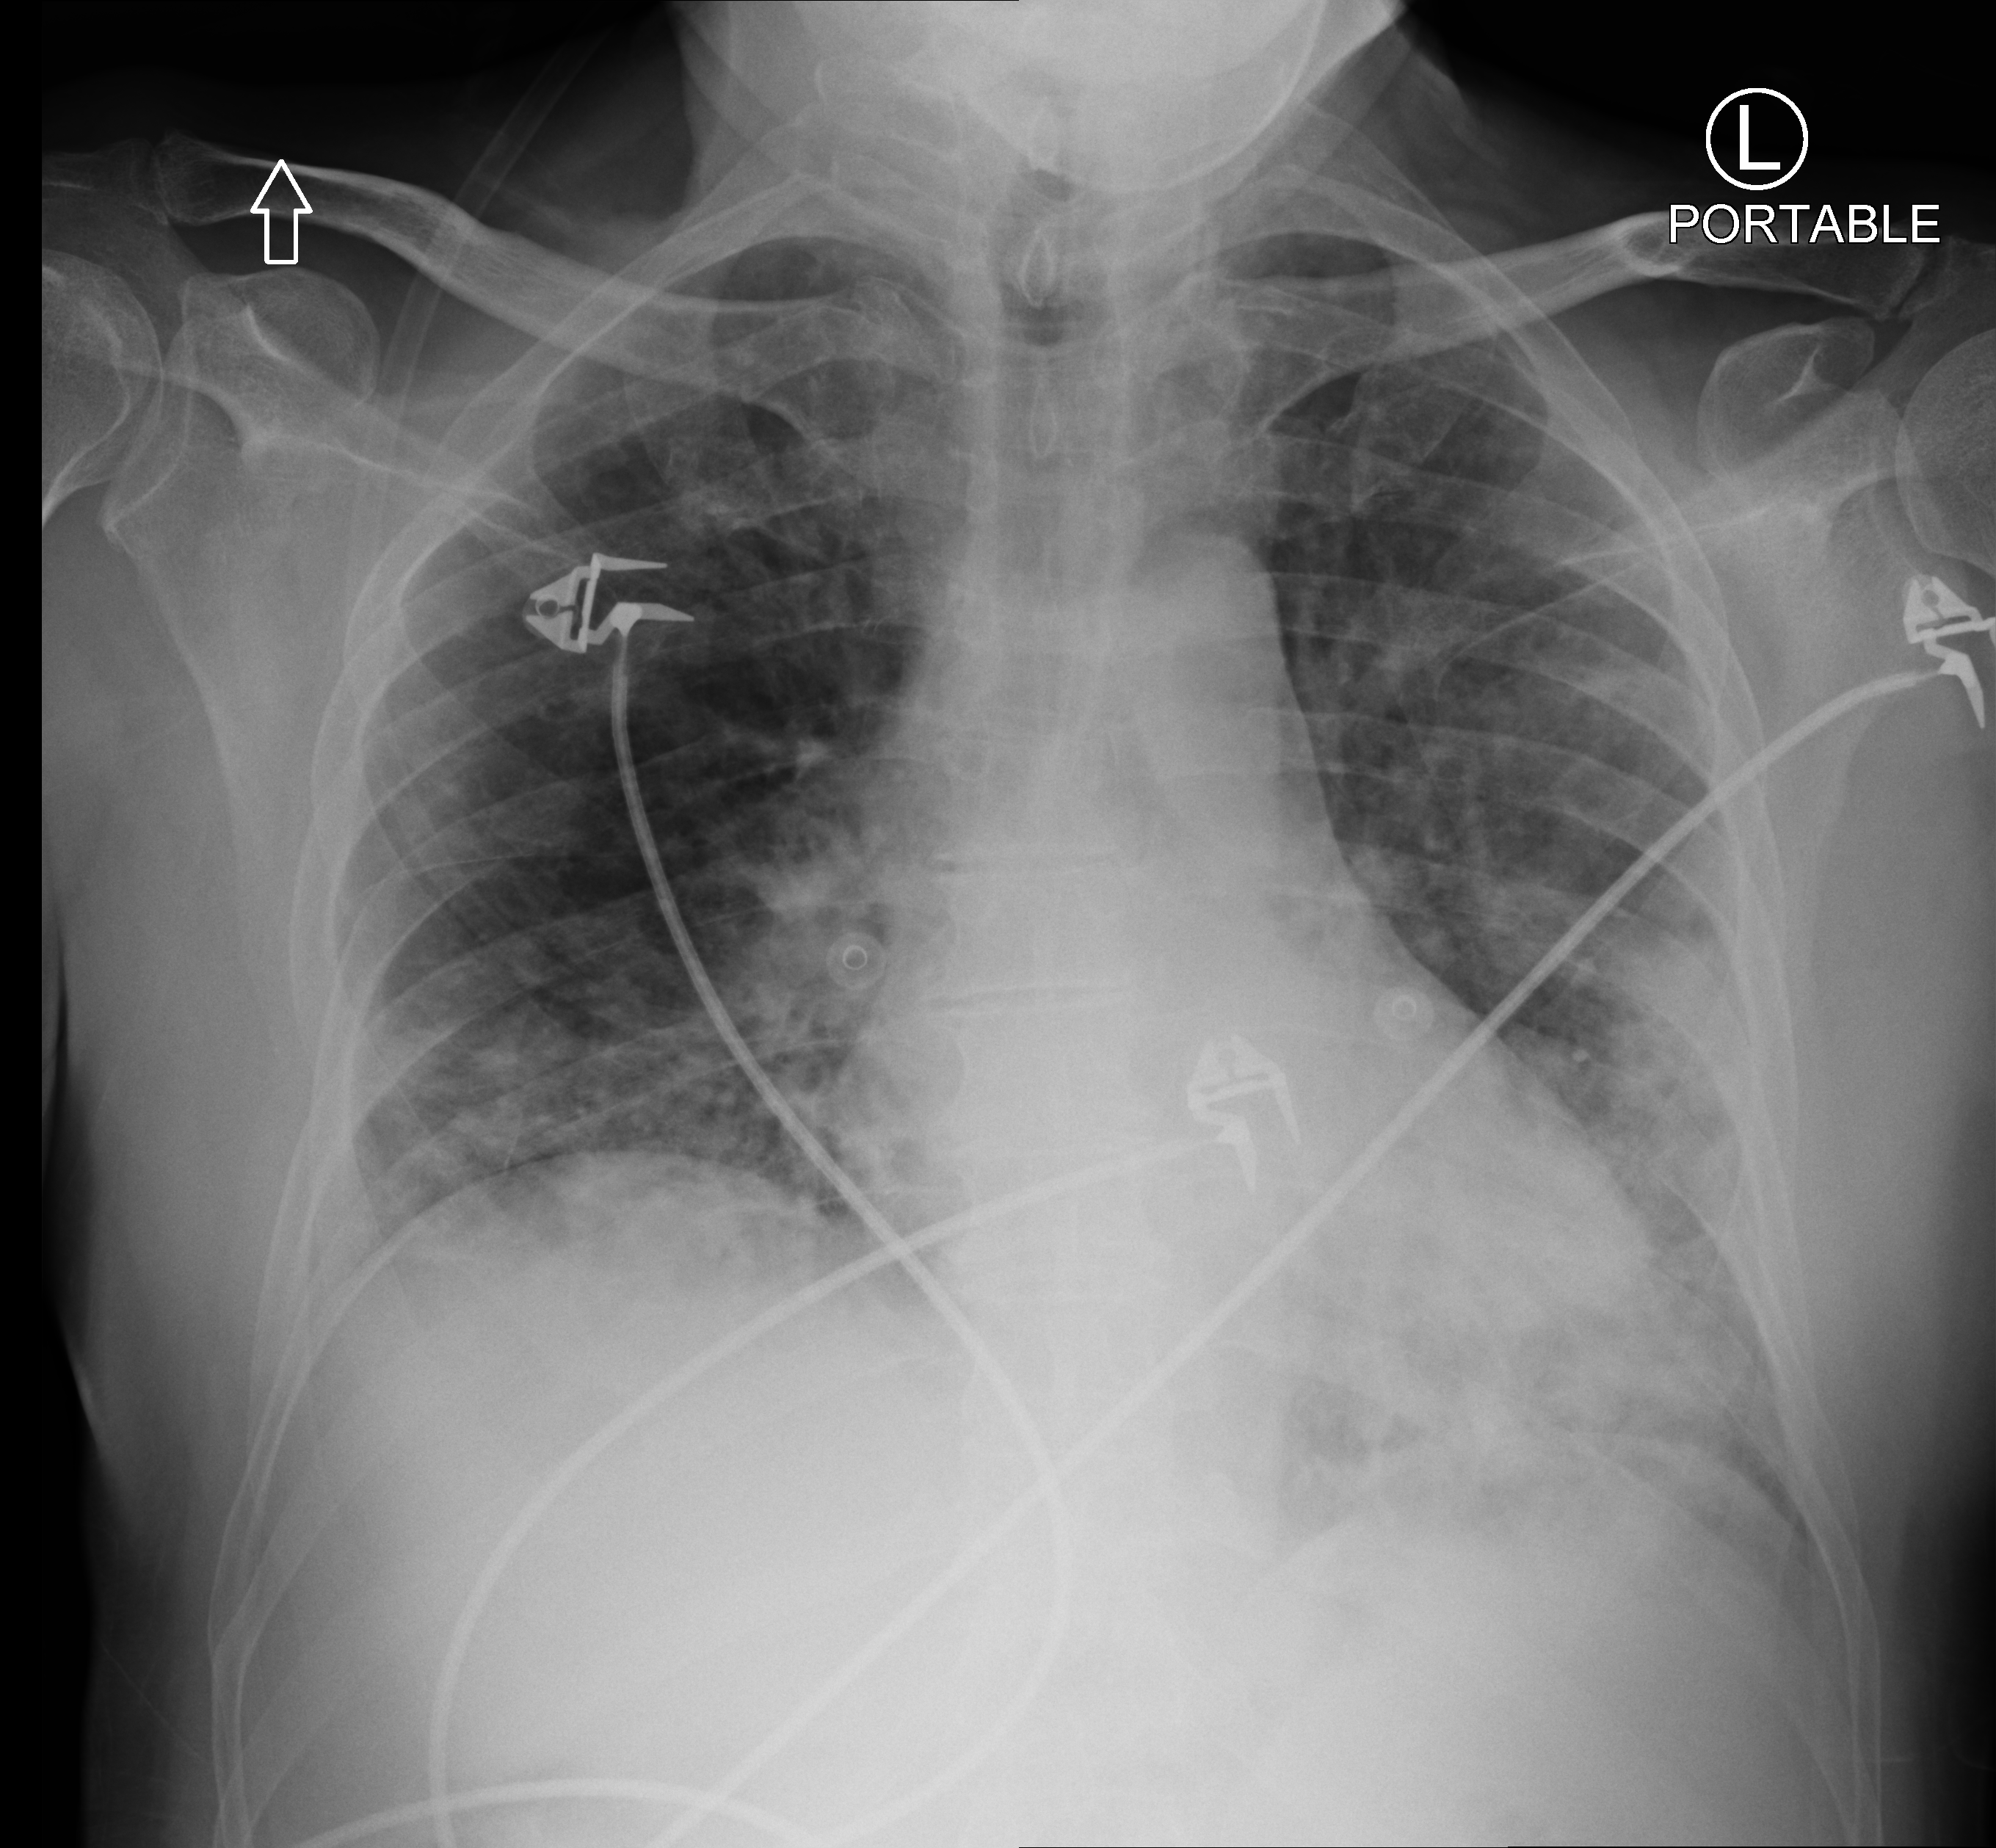
Bedside chest radiograph (computed radiography), anteroposterior (AP) projection. Patient hospitalised with COVID-19; male, aged 60–74 years.
From the hospital-stay record, not from the radiograph (when in the stay this image was taken is not recorded):
- length of hospital stay: 12 days